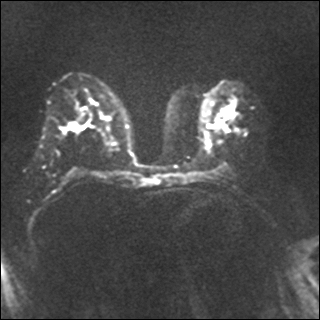
Breast MRI, one axial slice. Position 21 of 35 along the scan axis. Diffusion-weighted series; image 2 of 4 stored at this slice position (different b-values; order by instance number). 1.5 T. 4 mm slice thickness. 320 × 320 image matrix, field of view 320 × 320 mm. Female patient.
Structures marked on this image (expert manual segmentation):
- tumour on diffusion-weighted imaging: bounding box <227,114,230,118> (left, top, right, bottom; pixels)